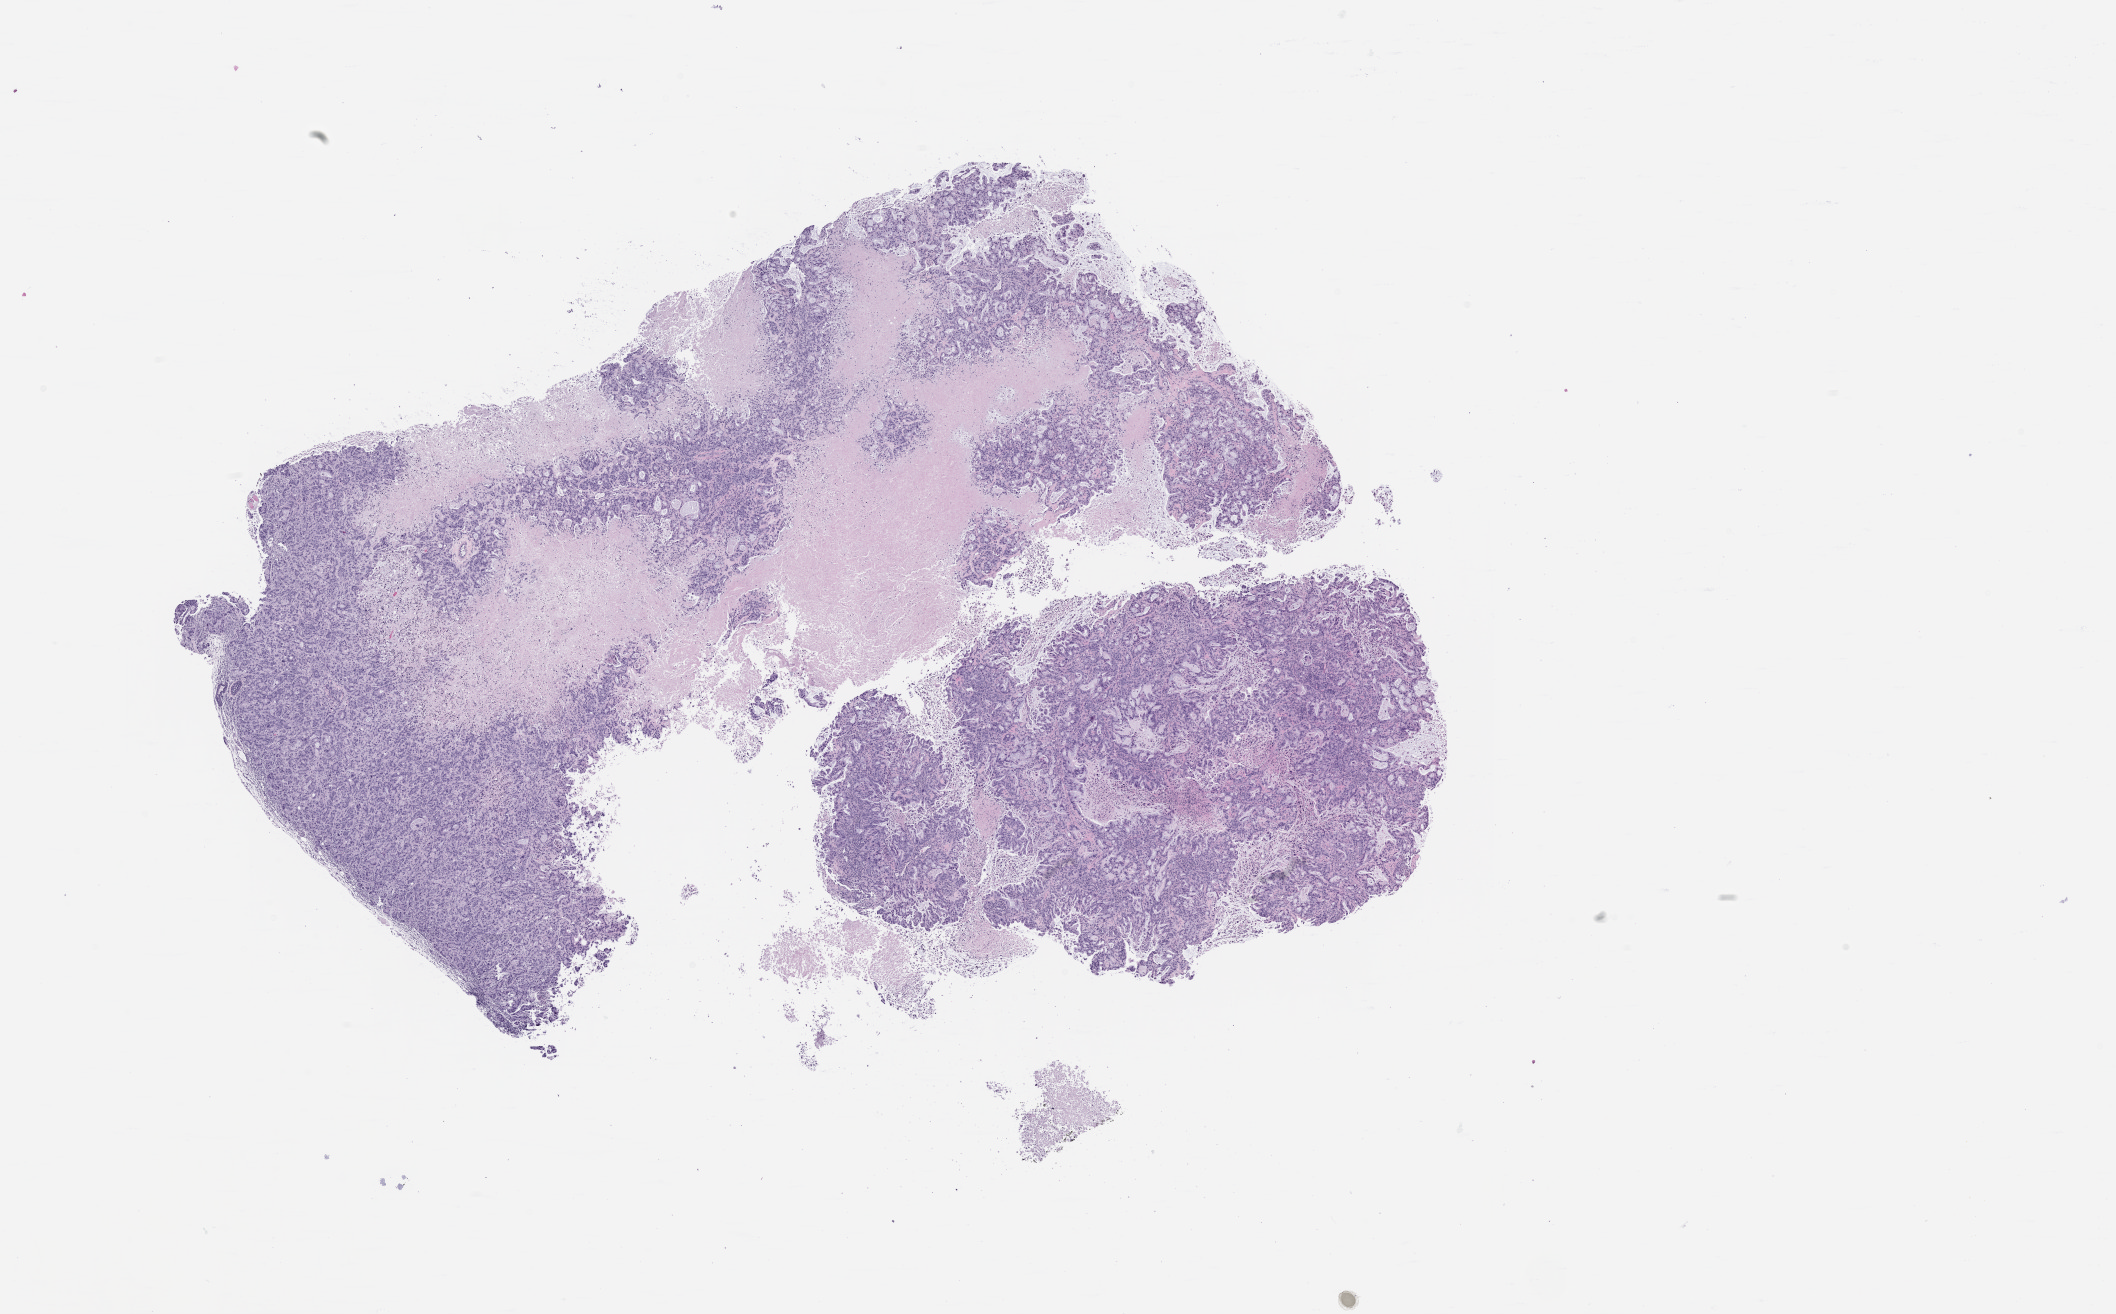
H&E whole-slide image of a patient-derived xenograft (PDX) tumor grown in a mouse, passage 2, a low-resolution overview of the entire scanned area, about 17.0 x 10.6 mm, FFPE section, tumor site category: pancreas.
* originating patient diagnosis: Pancreatic Adenocarcinoma